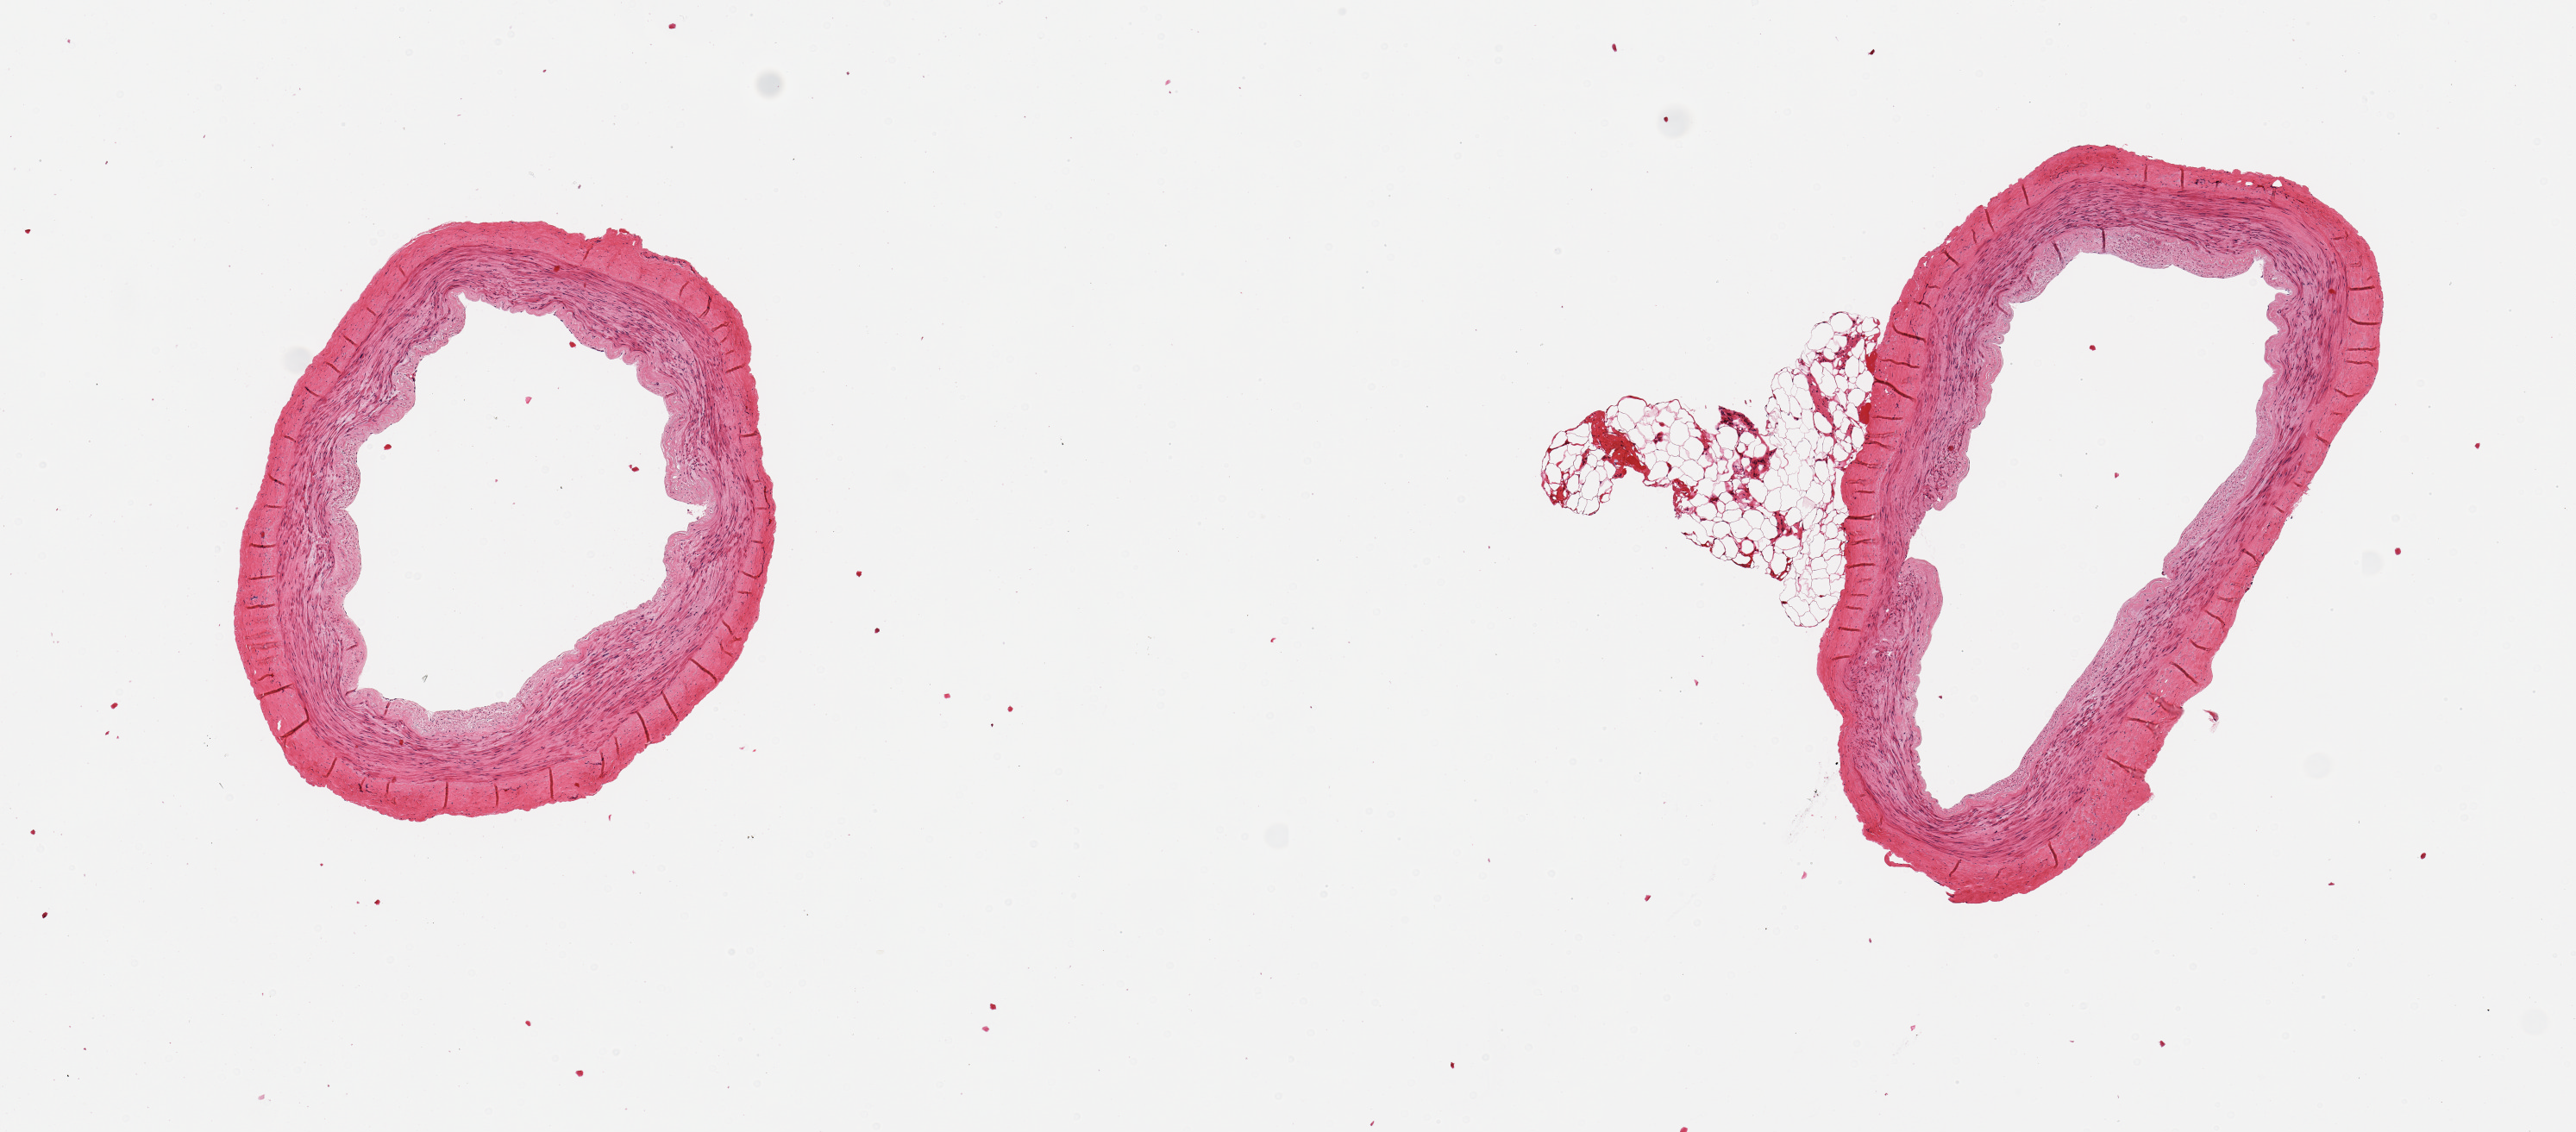
Whole-slide image, H&E stain — whole scanned area (about 11.8 x 5.2 mm) shown as a low-resolution overview. PAXgene-fixed, paraffin-embedded tissue. Section of tibial artery (target tissue). Tissue donor sample. Donor sex: male.
Reviewer comment on this tissue sample: 2 pieces; intimal thickening, small attachment of fat.